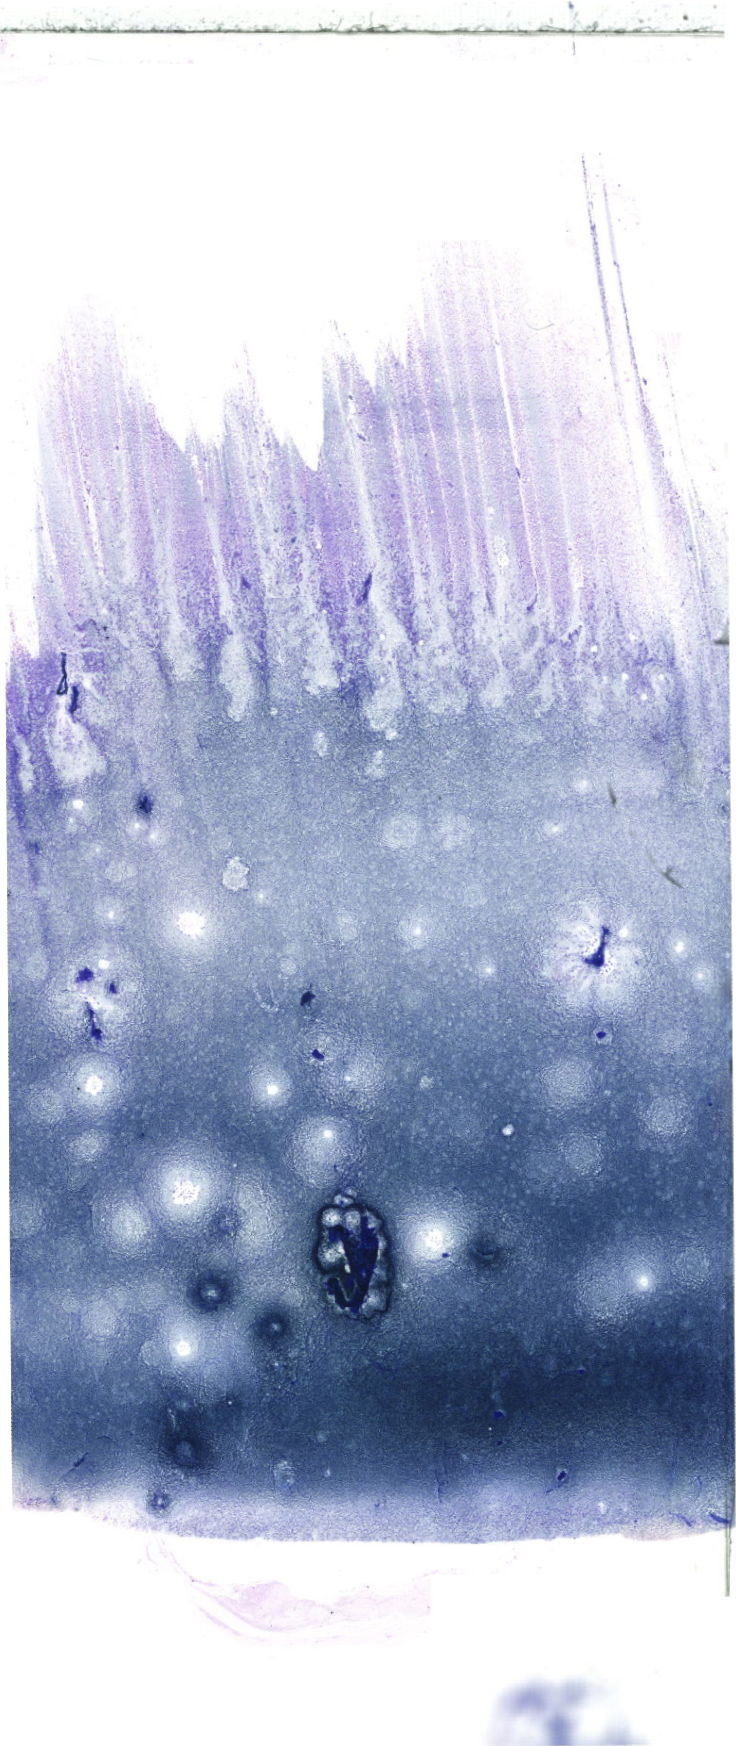
May-Grünwald-Giemsa (MGG)-stained marrow aspirate smear (whole slide) — low-resolution overview of the scanned area, about 20.9 x 49.5 mm. Patient sex: male.
Diagnosis: Acute Monocytic Leukemia.